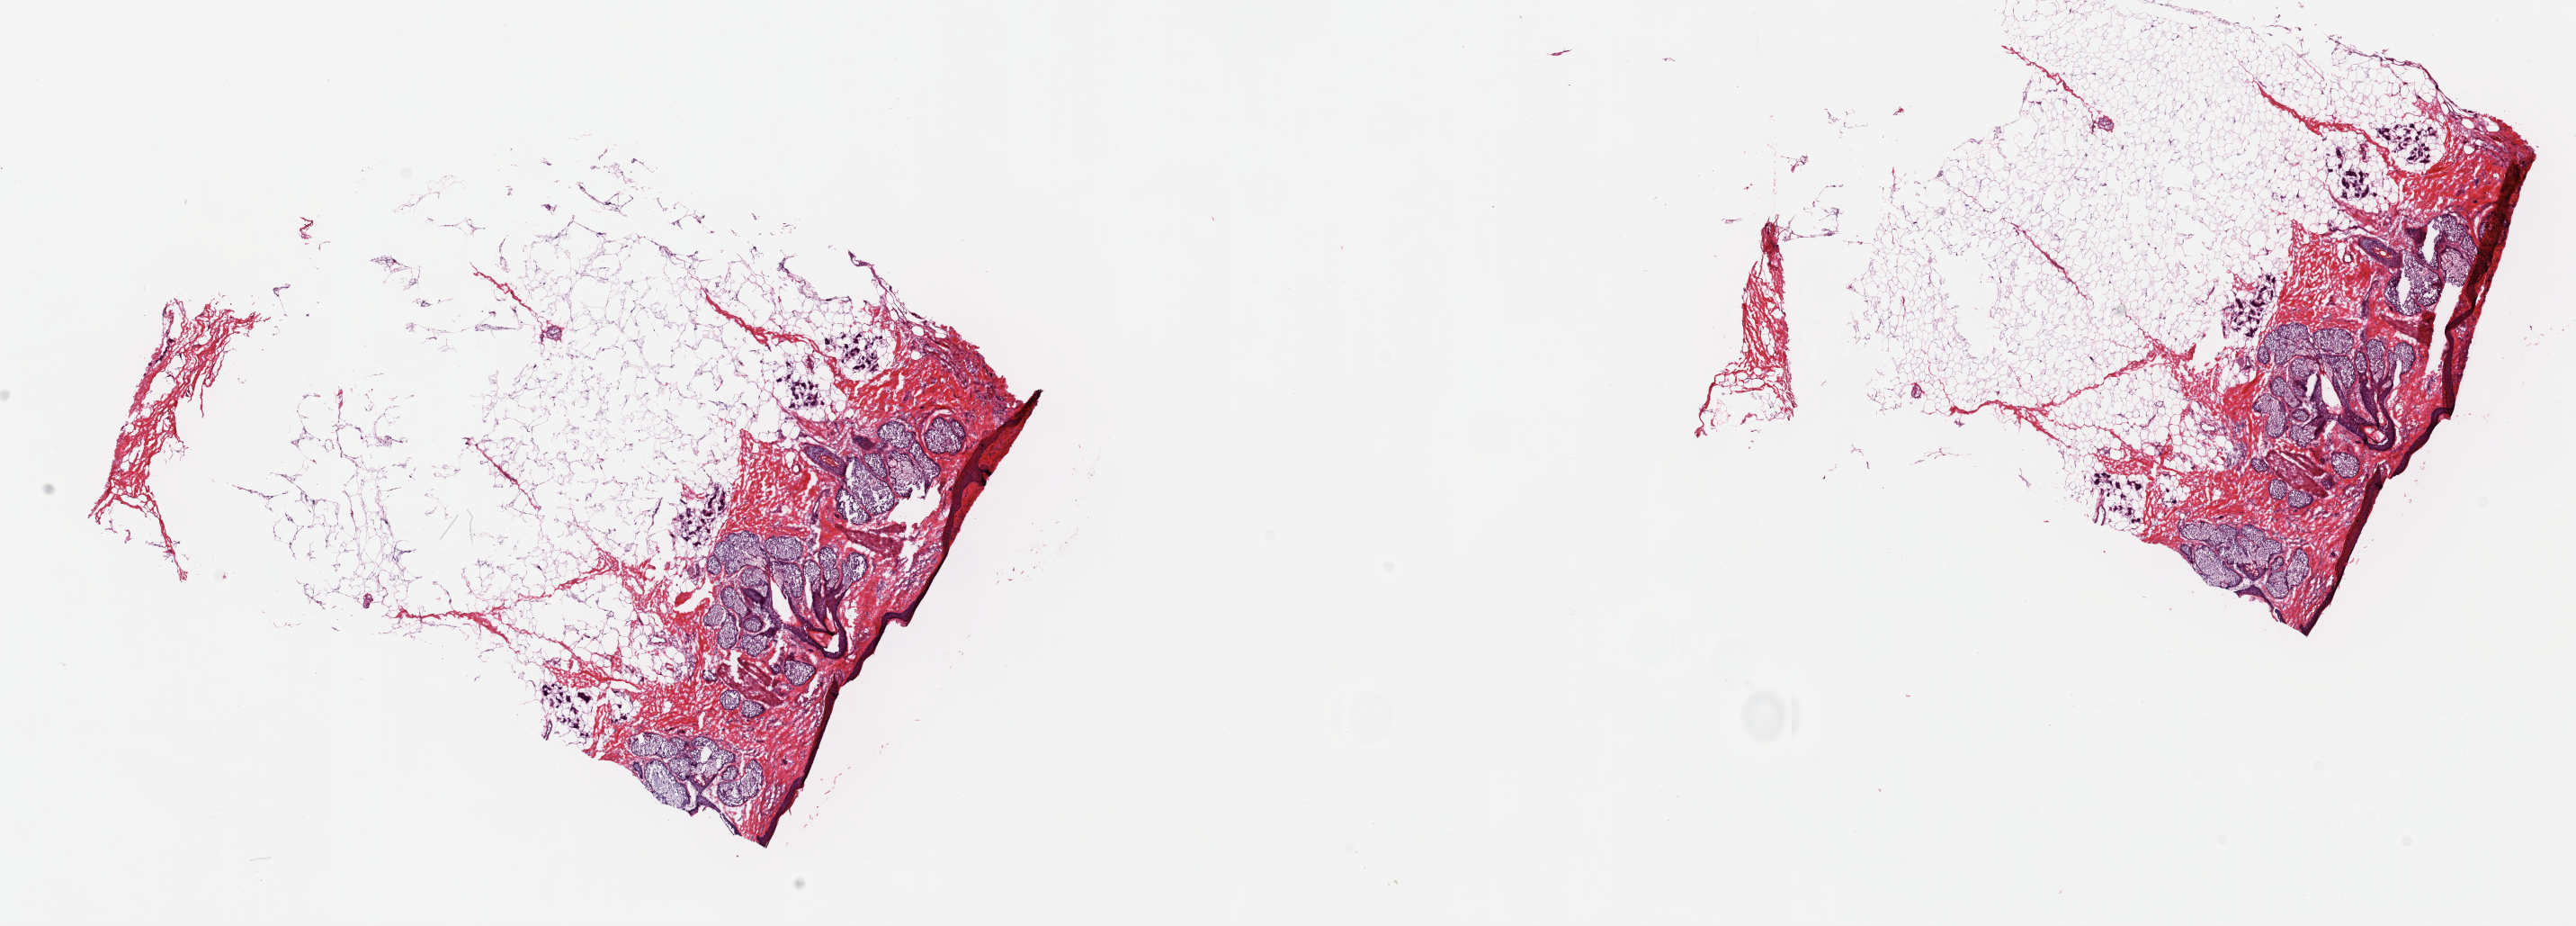
Digitized H&E tissue section (whole slide), a low-resolution overview of the entire scanned area, about 23.1 x 8.3 mm, frozen section from the top of the tissue portion, solid tissue normal (non-tumour tissue) sample from the connective, subcutaneous and other soft tissues. Patient: male, age at initial diagnosis 75 years. Pathologist review of this section (percent, as recorded): tumour cells 0%, tumour nuclei 0%.
This section: solid tissue normal sample (biorepository sample class). Patient diagnosis: Undifferentiated sarcoma (connective, subcutaneous and other soft tissues of head, face, and neck).